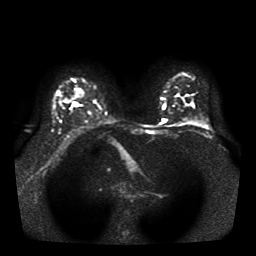
Breast MRI, one axial slice; position 27 of 41 along the scan axis; diffusion-weighted series; image 2 of 4 stored at this slice position (different b-values; order by instance number); 1.5 T; 5 mm slice thickness; 256 × 256 image matrix. Female patient.
Outlined on this slice (outlined manually by an expert reader):
- tumour on diffusion-weighted imaging: box from (x=71, y=103) to (x=82, y=109) px